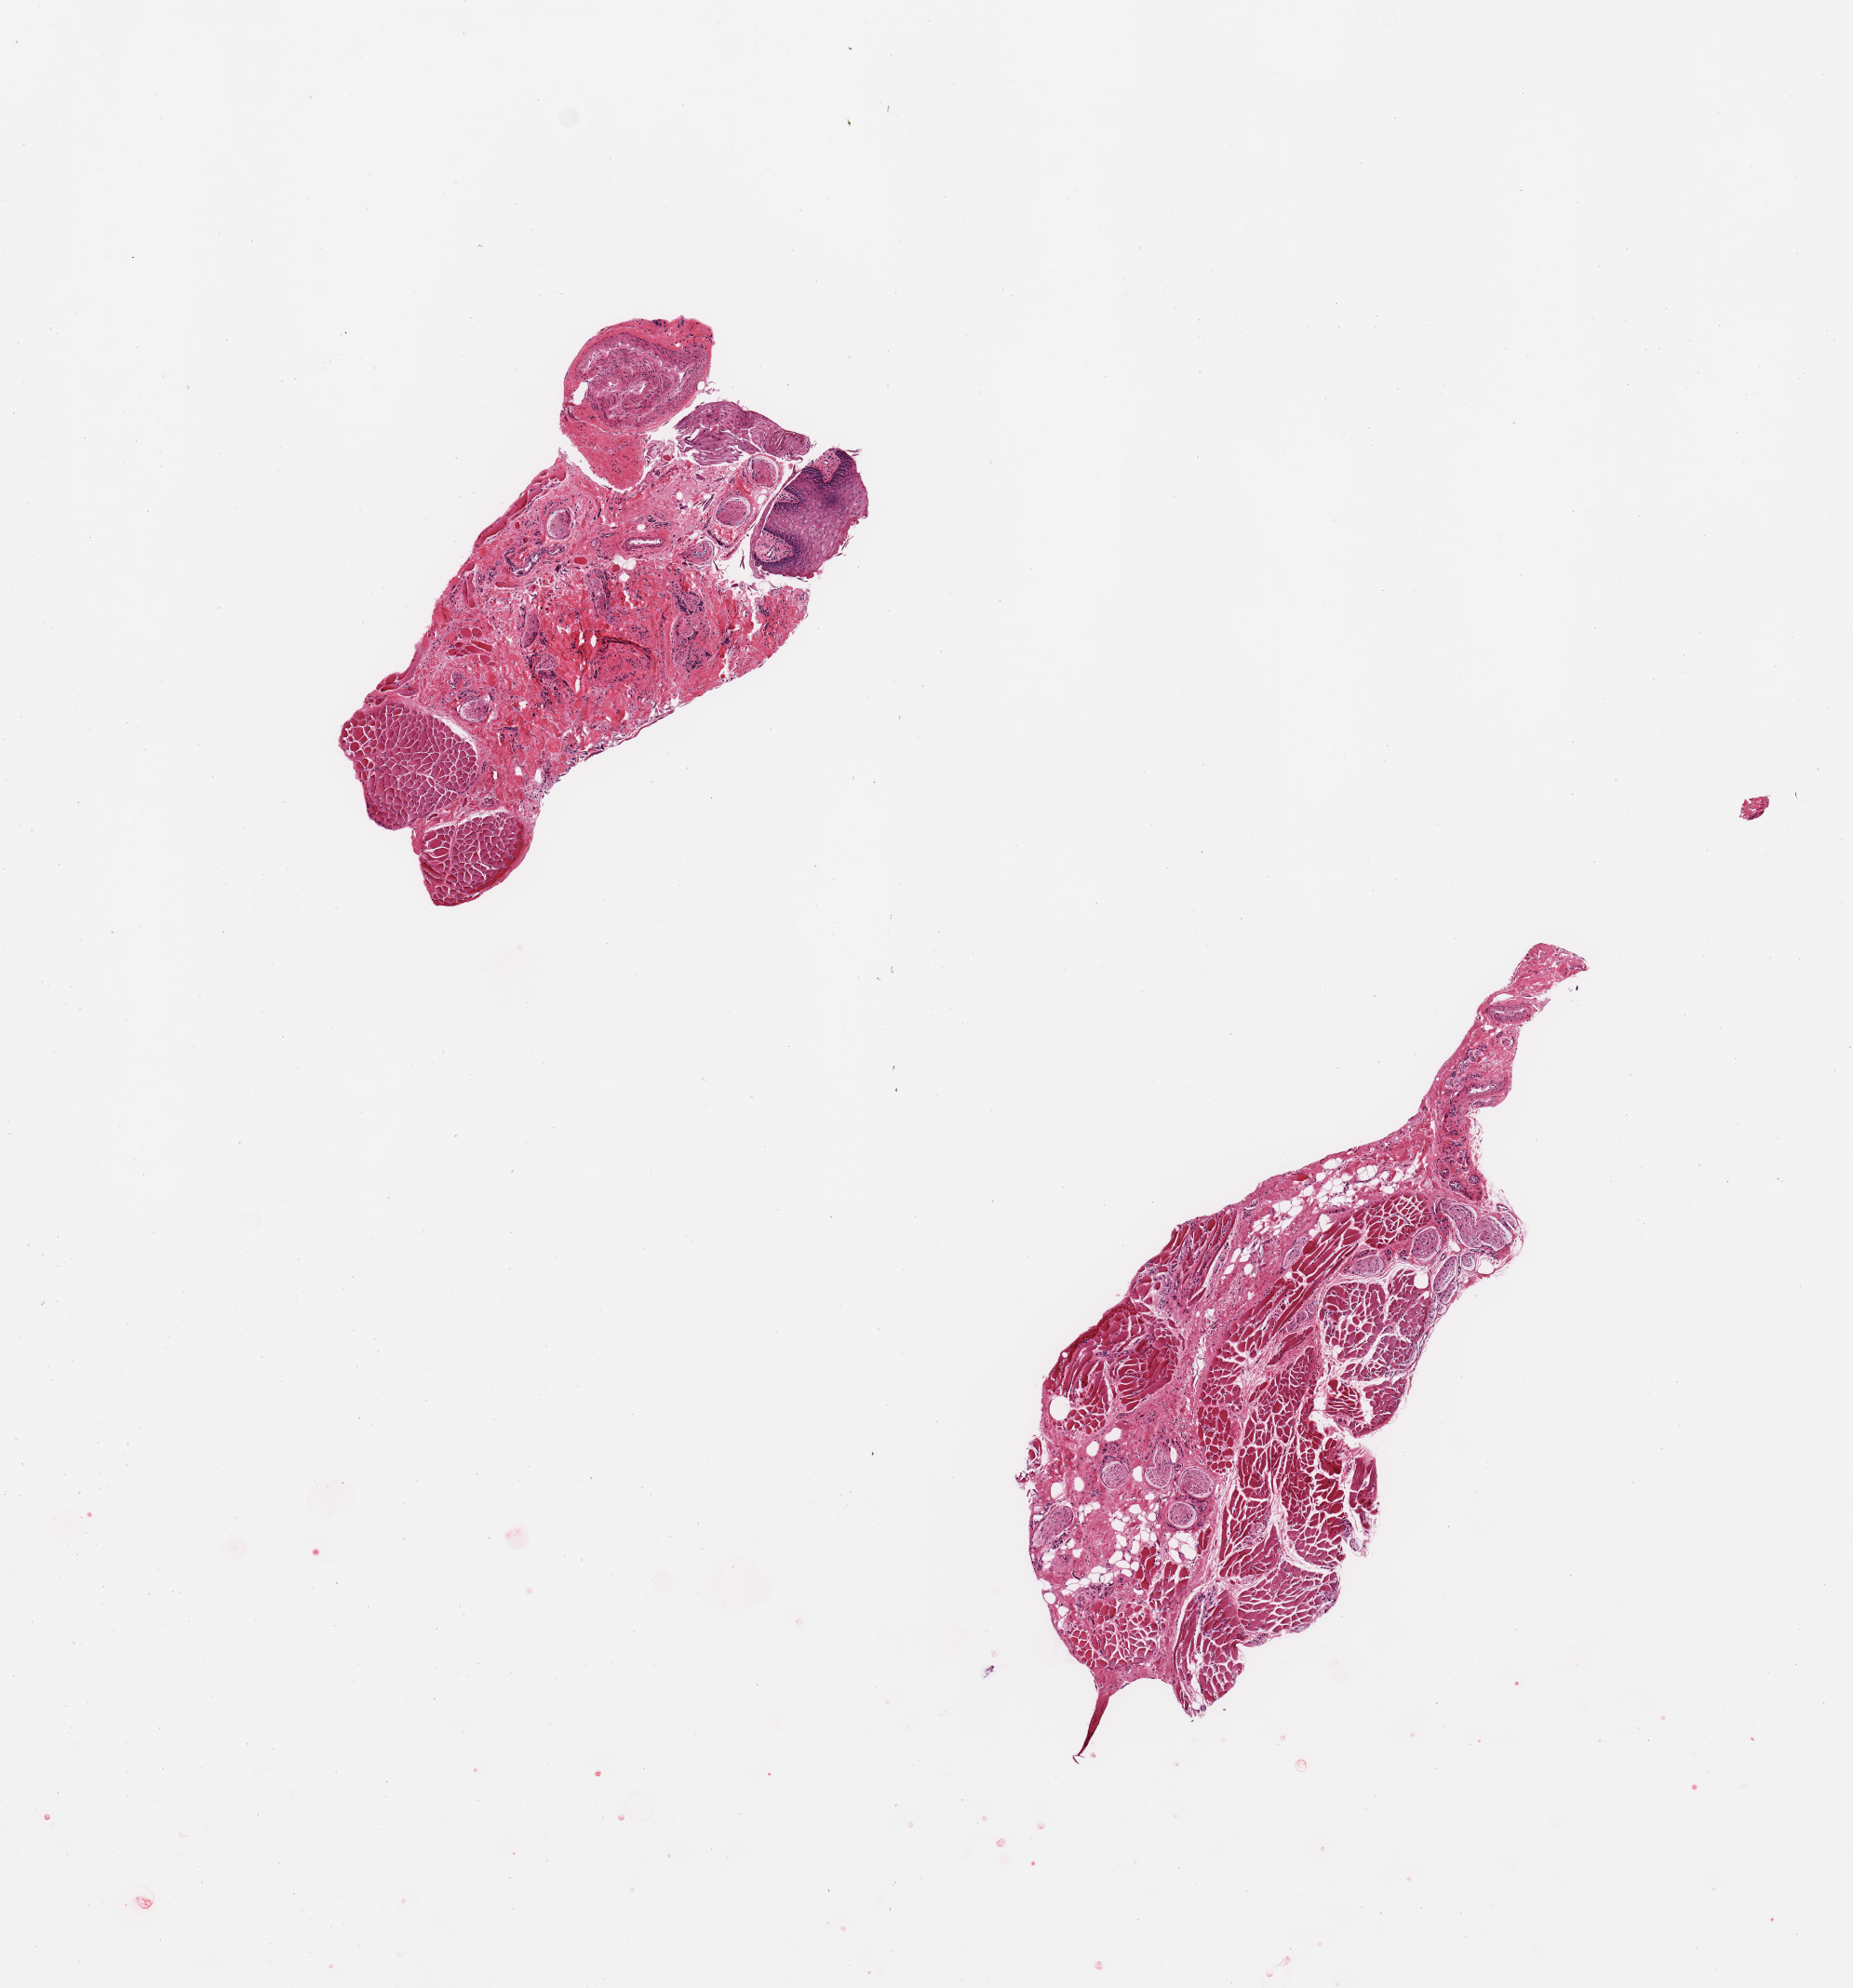
H&E whole-slide image, whole scanned area (about 7.9 x 8.4 mm, from a 20x scan) shown as a low-resolution overview, PAXgene-fixed paraffin-embedded (PFPE) section, target tissue: minor salivary gland, donor tissue sample.
Pathologist's review note for this sample: 2 pieces; mostly skeletal muscle fibers, nerves and fibrovascular tissue with focal small fragment of squamous epithelium; no target tissue observed.